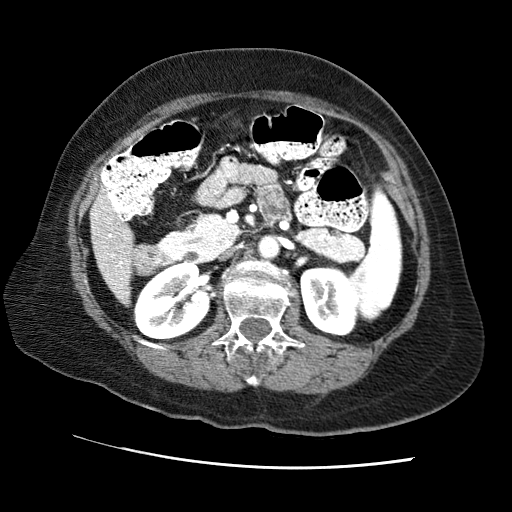
Contrast-enhanced abdominal CT (liver protocol), one axial slice; slice 19 of 65 in the series (ordered by position); 120 kVp; soft-tissue window (W 400 / L 40 HU); 2.5 mm slice thickness; 512 × 512 image matrix. Case-level facts recorded for this patient, not image findings: diagnosis: hepatocellular carcinoma (patient treated with transarterial chemoembolisation; whether this scan precedes or follows treatment is not stated here); TNM stage (as recorded): Stage-II; Child-Pugh class: A; tumour differentiation: no biopsy; tumour size: 2.5 cm.
Outlined on this slice (semi-automatically segmented with operator editing):
- liver parenchyma outside the tumour (the mass and vessels are separate outlines, so this box may not span the whole liver): box from (x=90, y=194) to (x=132, y=304) px
- liver vessels: (x=95, y=207)–(x=128, y=294)